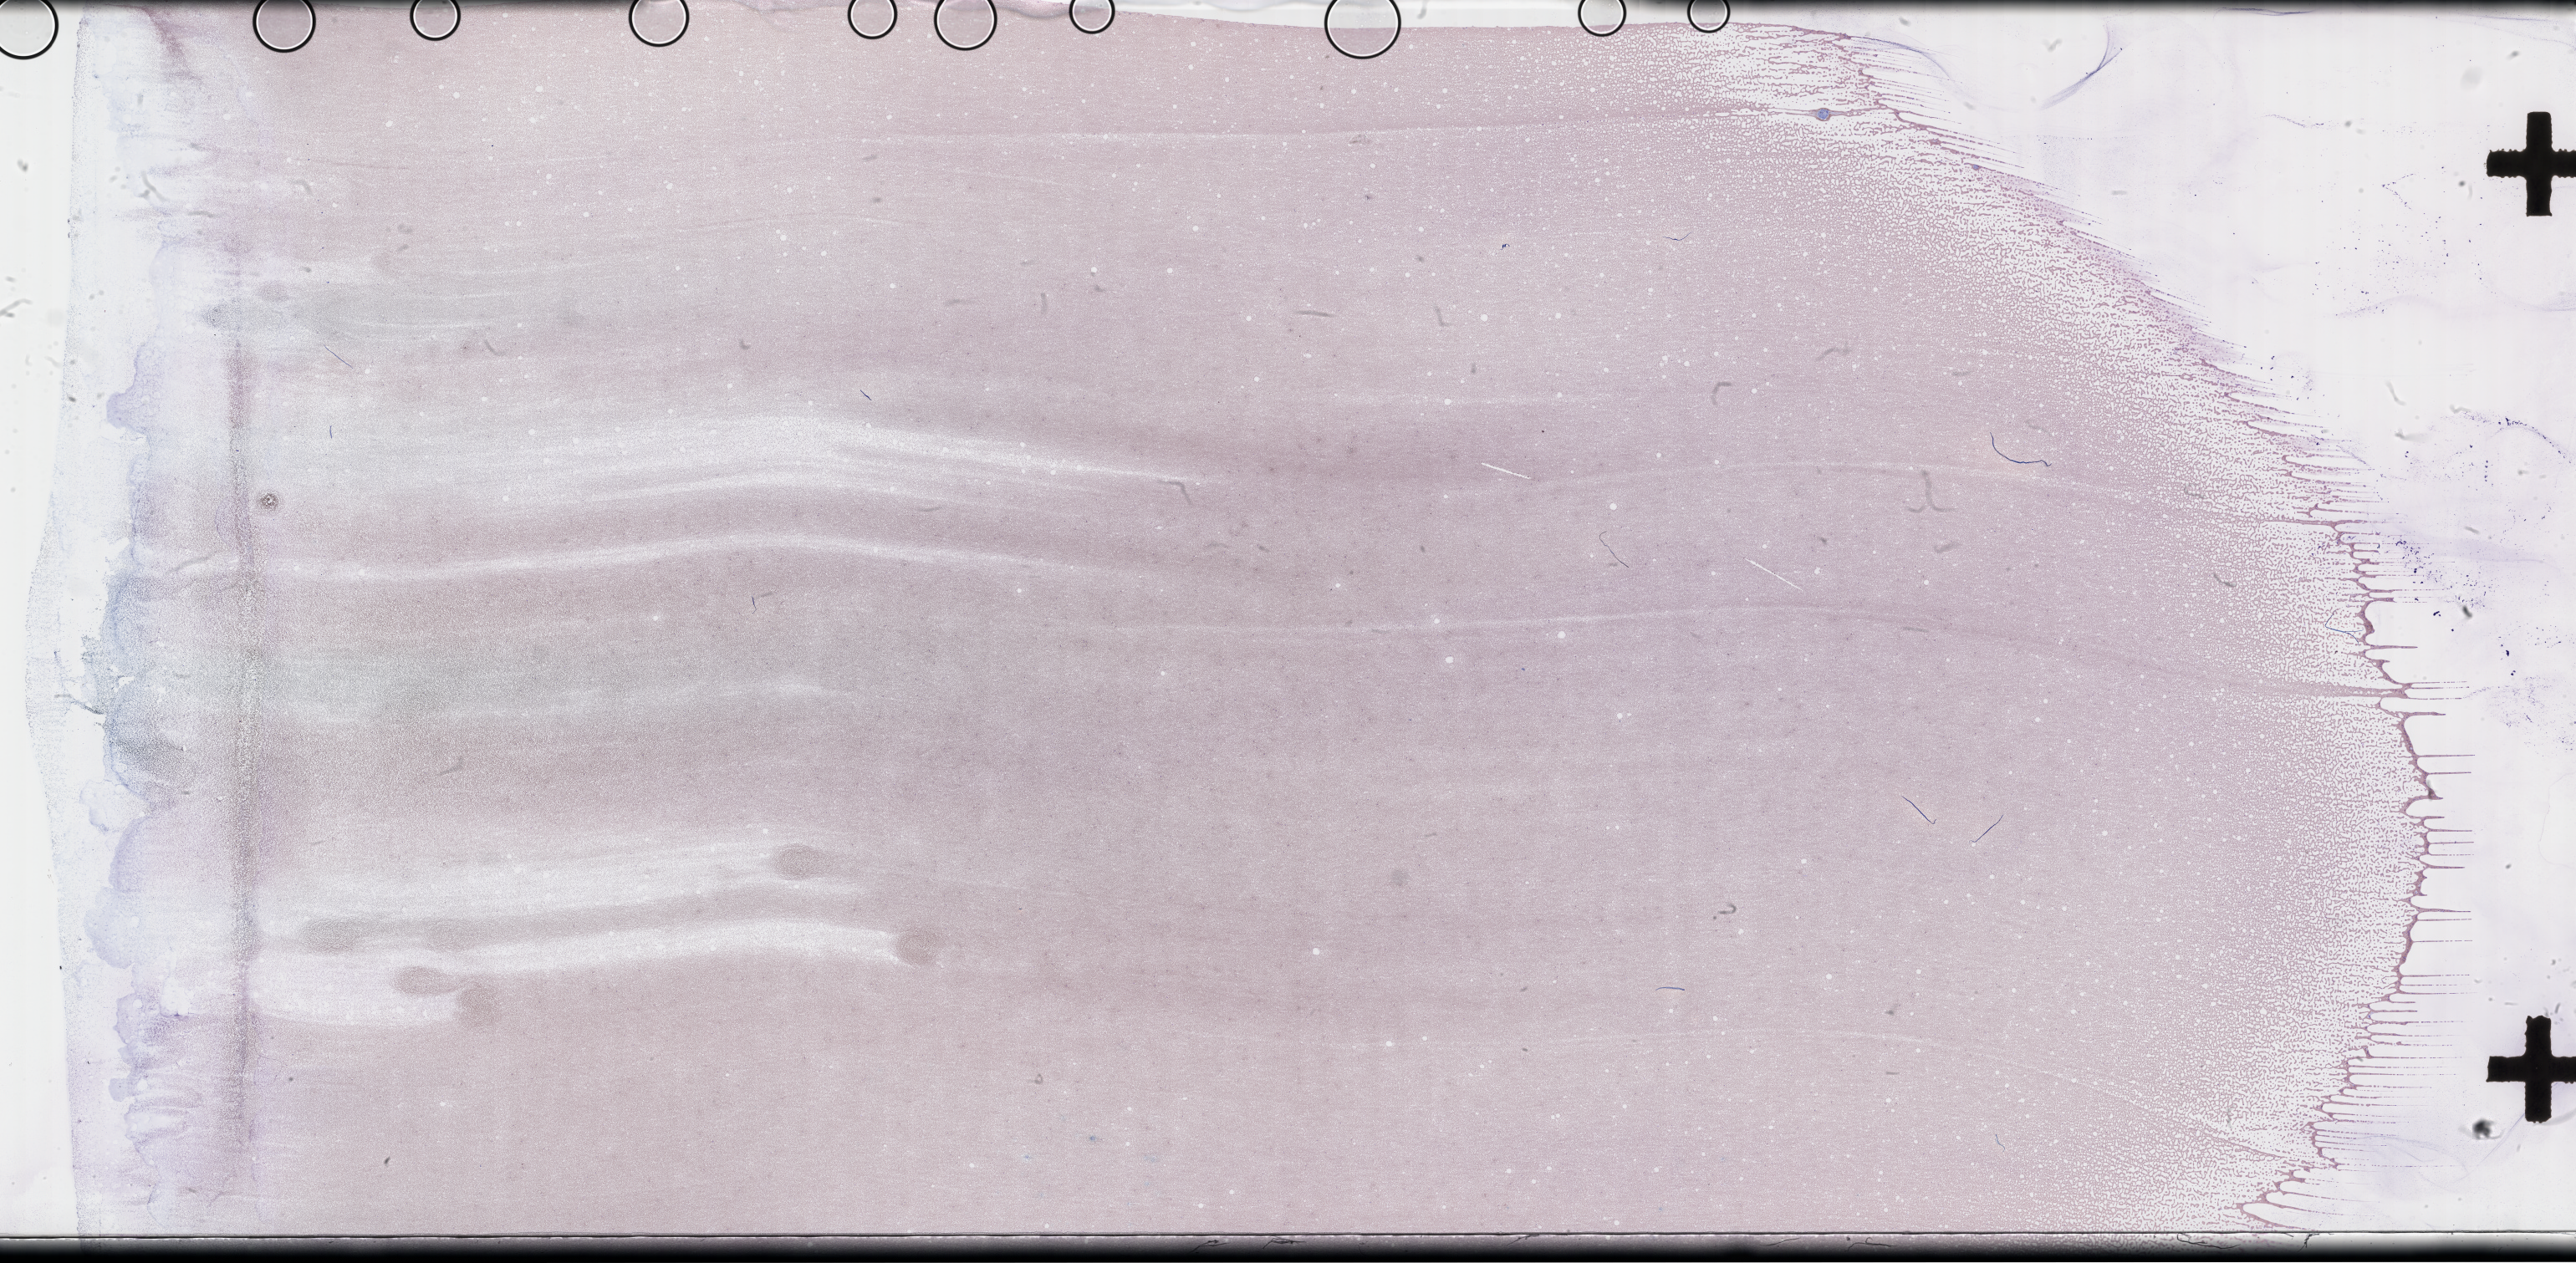
Wright-Giemsa-stained whole blood smear, whole-slide image, shown as a low-resolution overview of the whole scanned area (about 49.8 x 24.4 mm), smear from an EDTA sample. Female patient.
* patient diagnosis: Plasma Cell Myeloma